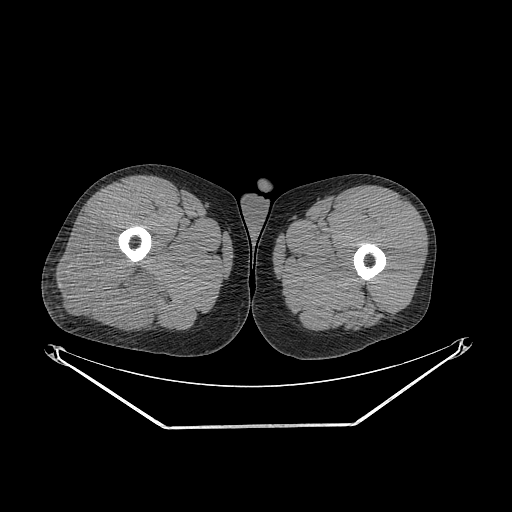
CT of an extremity soft-tissue mass (from a PET/CT study), one axial slice. Position 256 of 267 along the scan axis. Soft-tissue window (W 400 / L 40 HU). 3.75 mm slice thickness. 512 × 512 image matrix, field of view 500 × 500 mm. Male patient. Case-level facts recorded for this patient, not image findings: histological type: poorly differentiated synovial sarcoma; grade: high; site of the primary tumour: right buttock.
Structures marked on this image (expert contour drawn on MRI and transferred to this co-registered scan by the dataset authors):
- gross tumour volume including surrounding oedema: box from (x=55, y=217) to (x=159, y=330) px
- gross tumour volume (mass): (x=55, y=217)–(x=159, y=330)